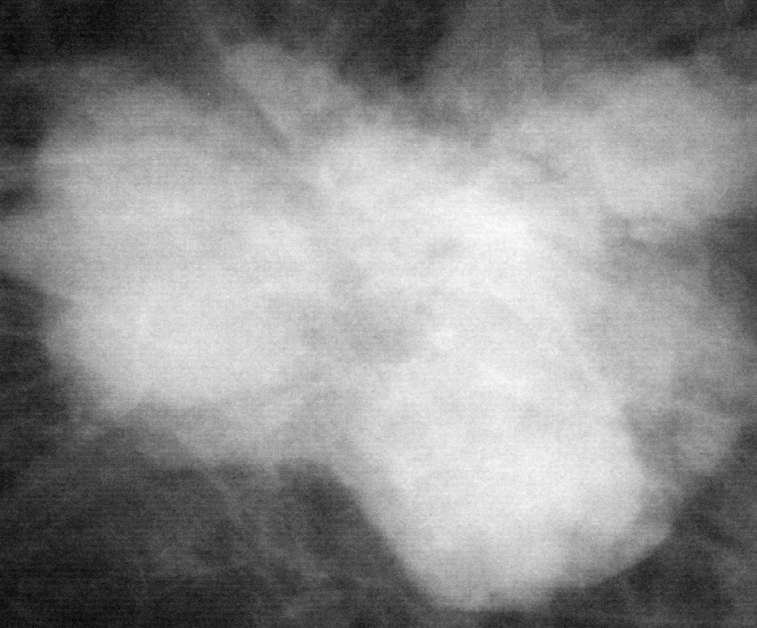
Cropped region of a digitized screen-film mammogram centred on a radiologist-marked abnormality, left breast, CC view.
- Mass, shape lobulated, margins microlobulated; BI-RADS assessment category 5; pathology (as recorded): malignant.